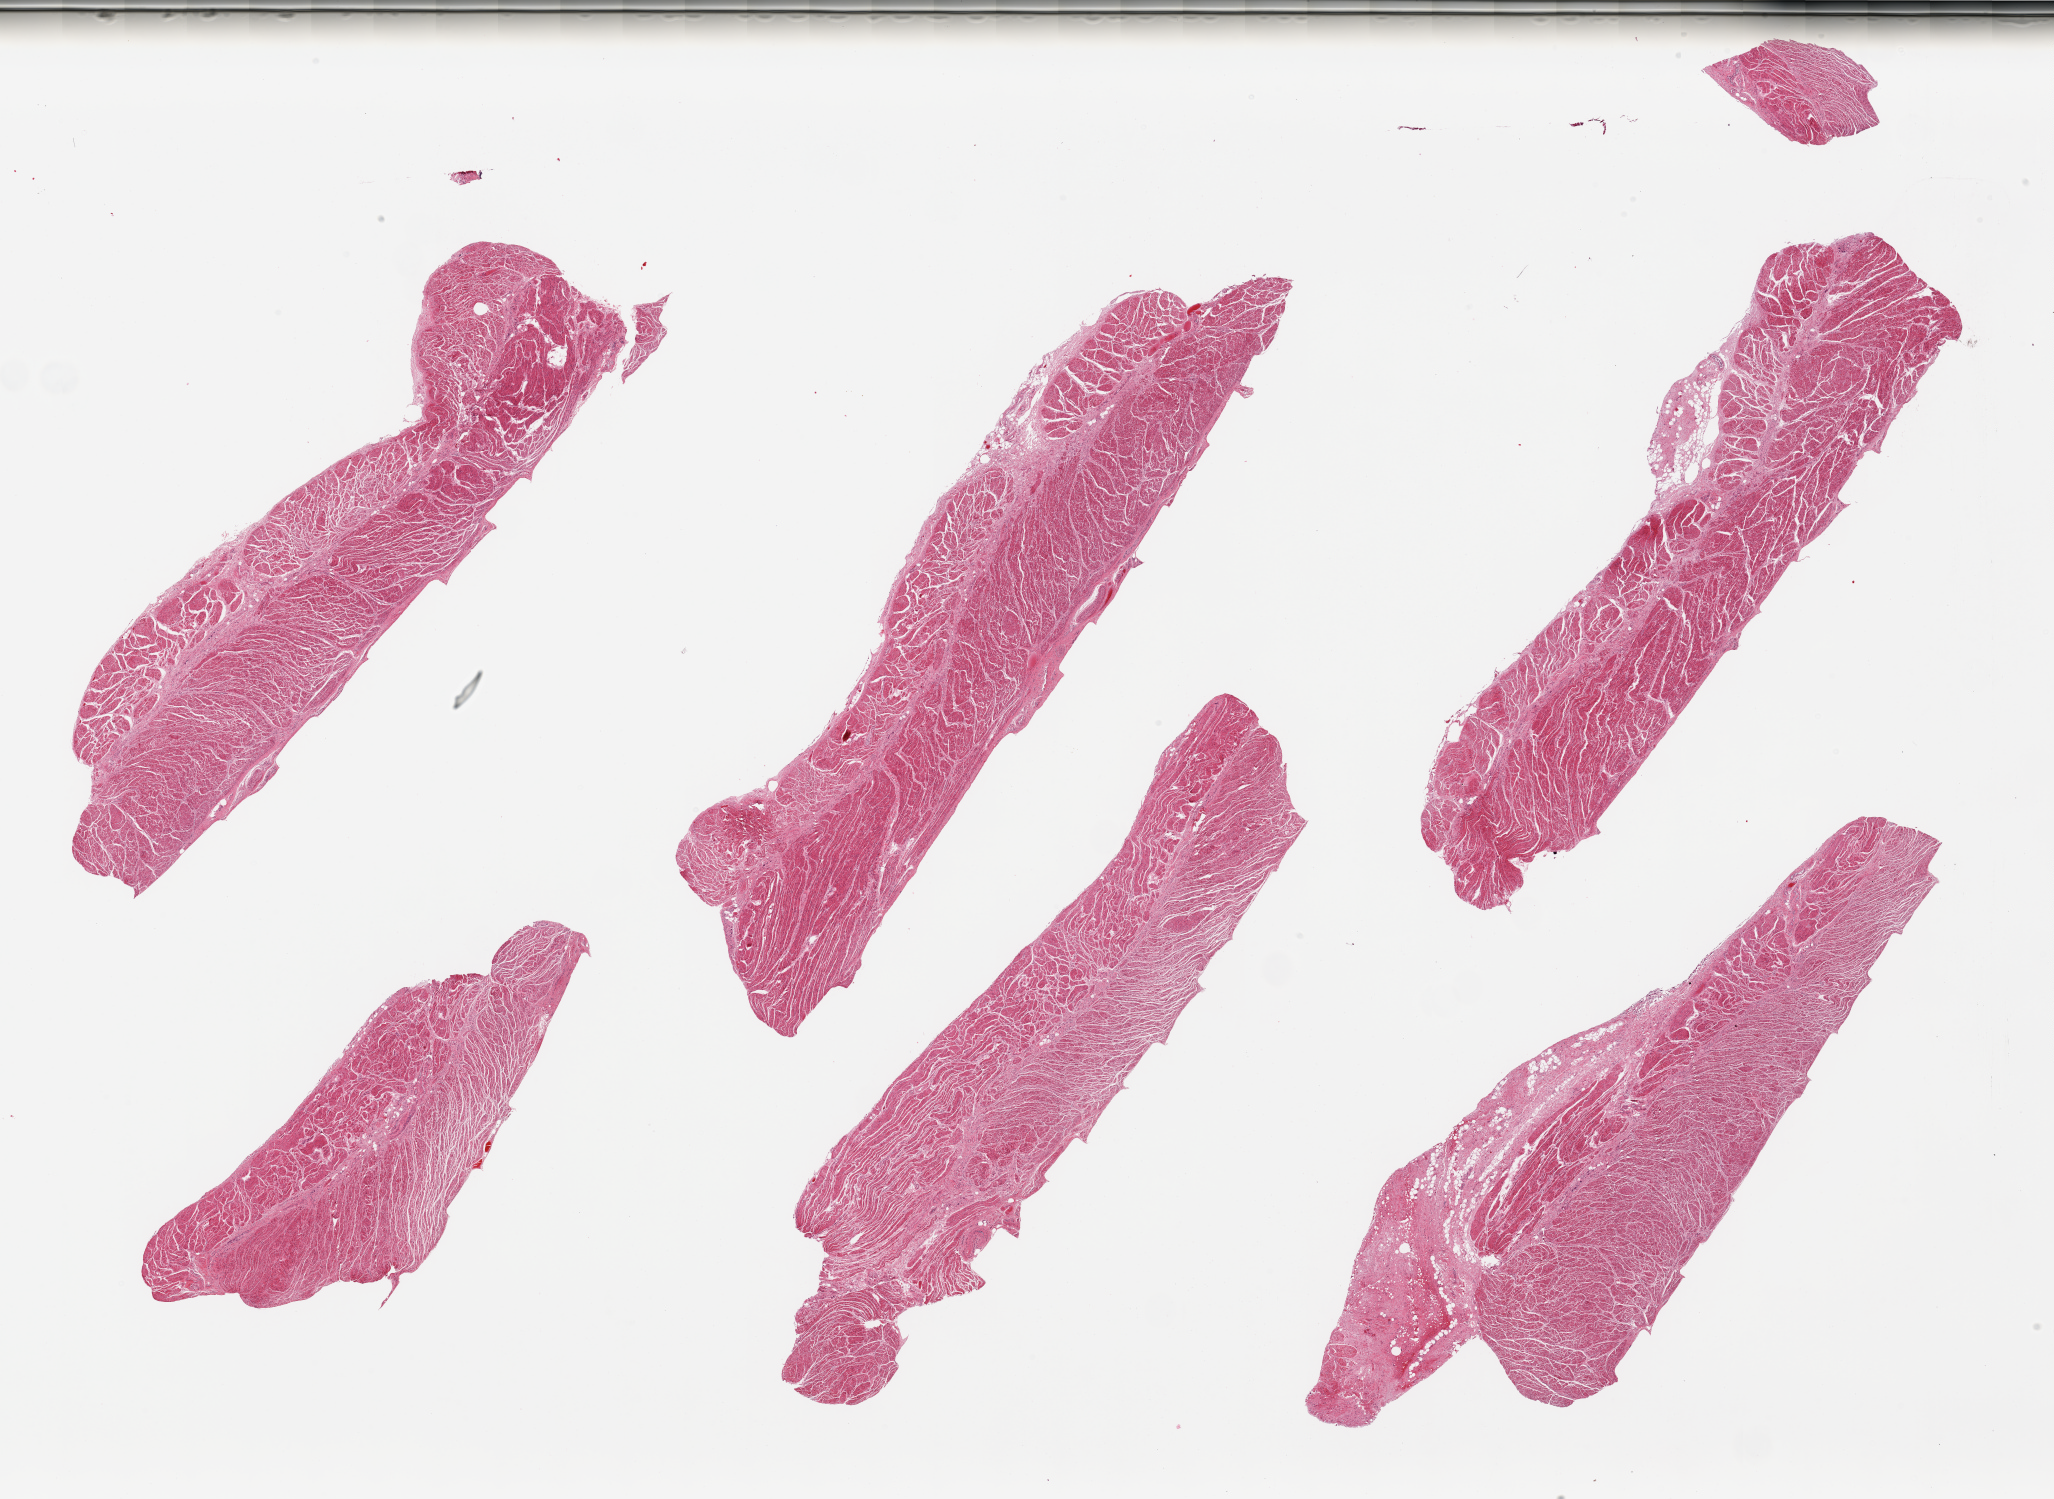
Hematoxylin and eosin (H&E) whole-slide image, brightfield — low-resolution overview of the scanned area, about 32.5 x 23.7 mm (slide scanned at 20x), PAXgene-fixed paraffin-embedded (PFPE) section, sampled site (target tissue): gastroesophageal junction, tissue donor sample.
- review note (as recorded): 6 pieces, all target muscularis